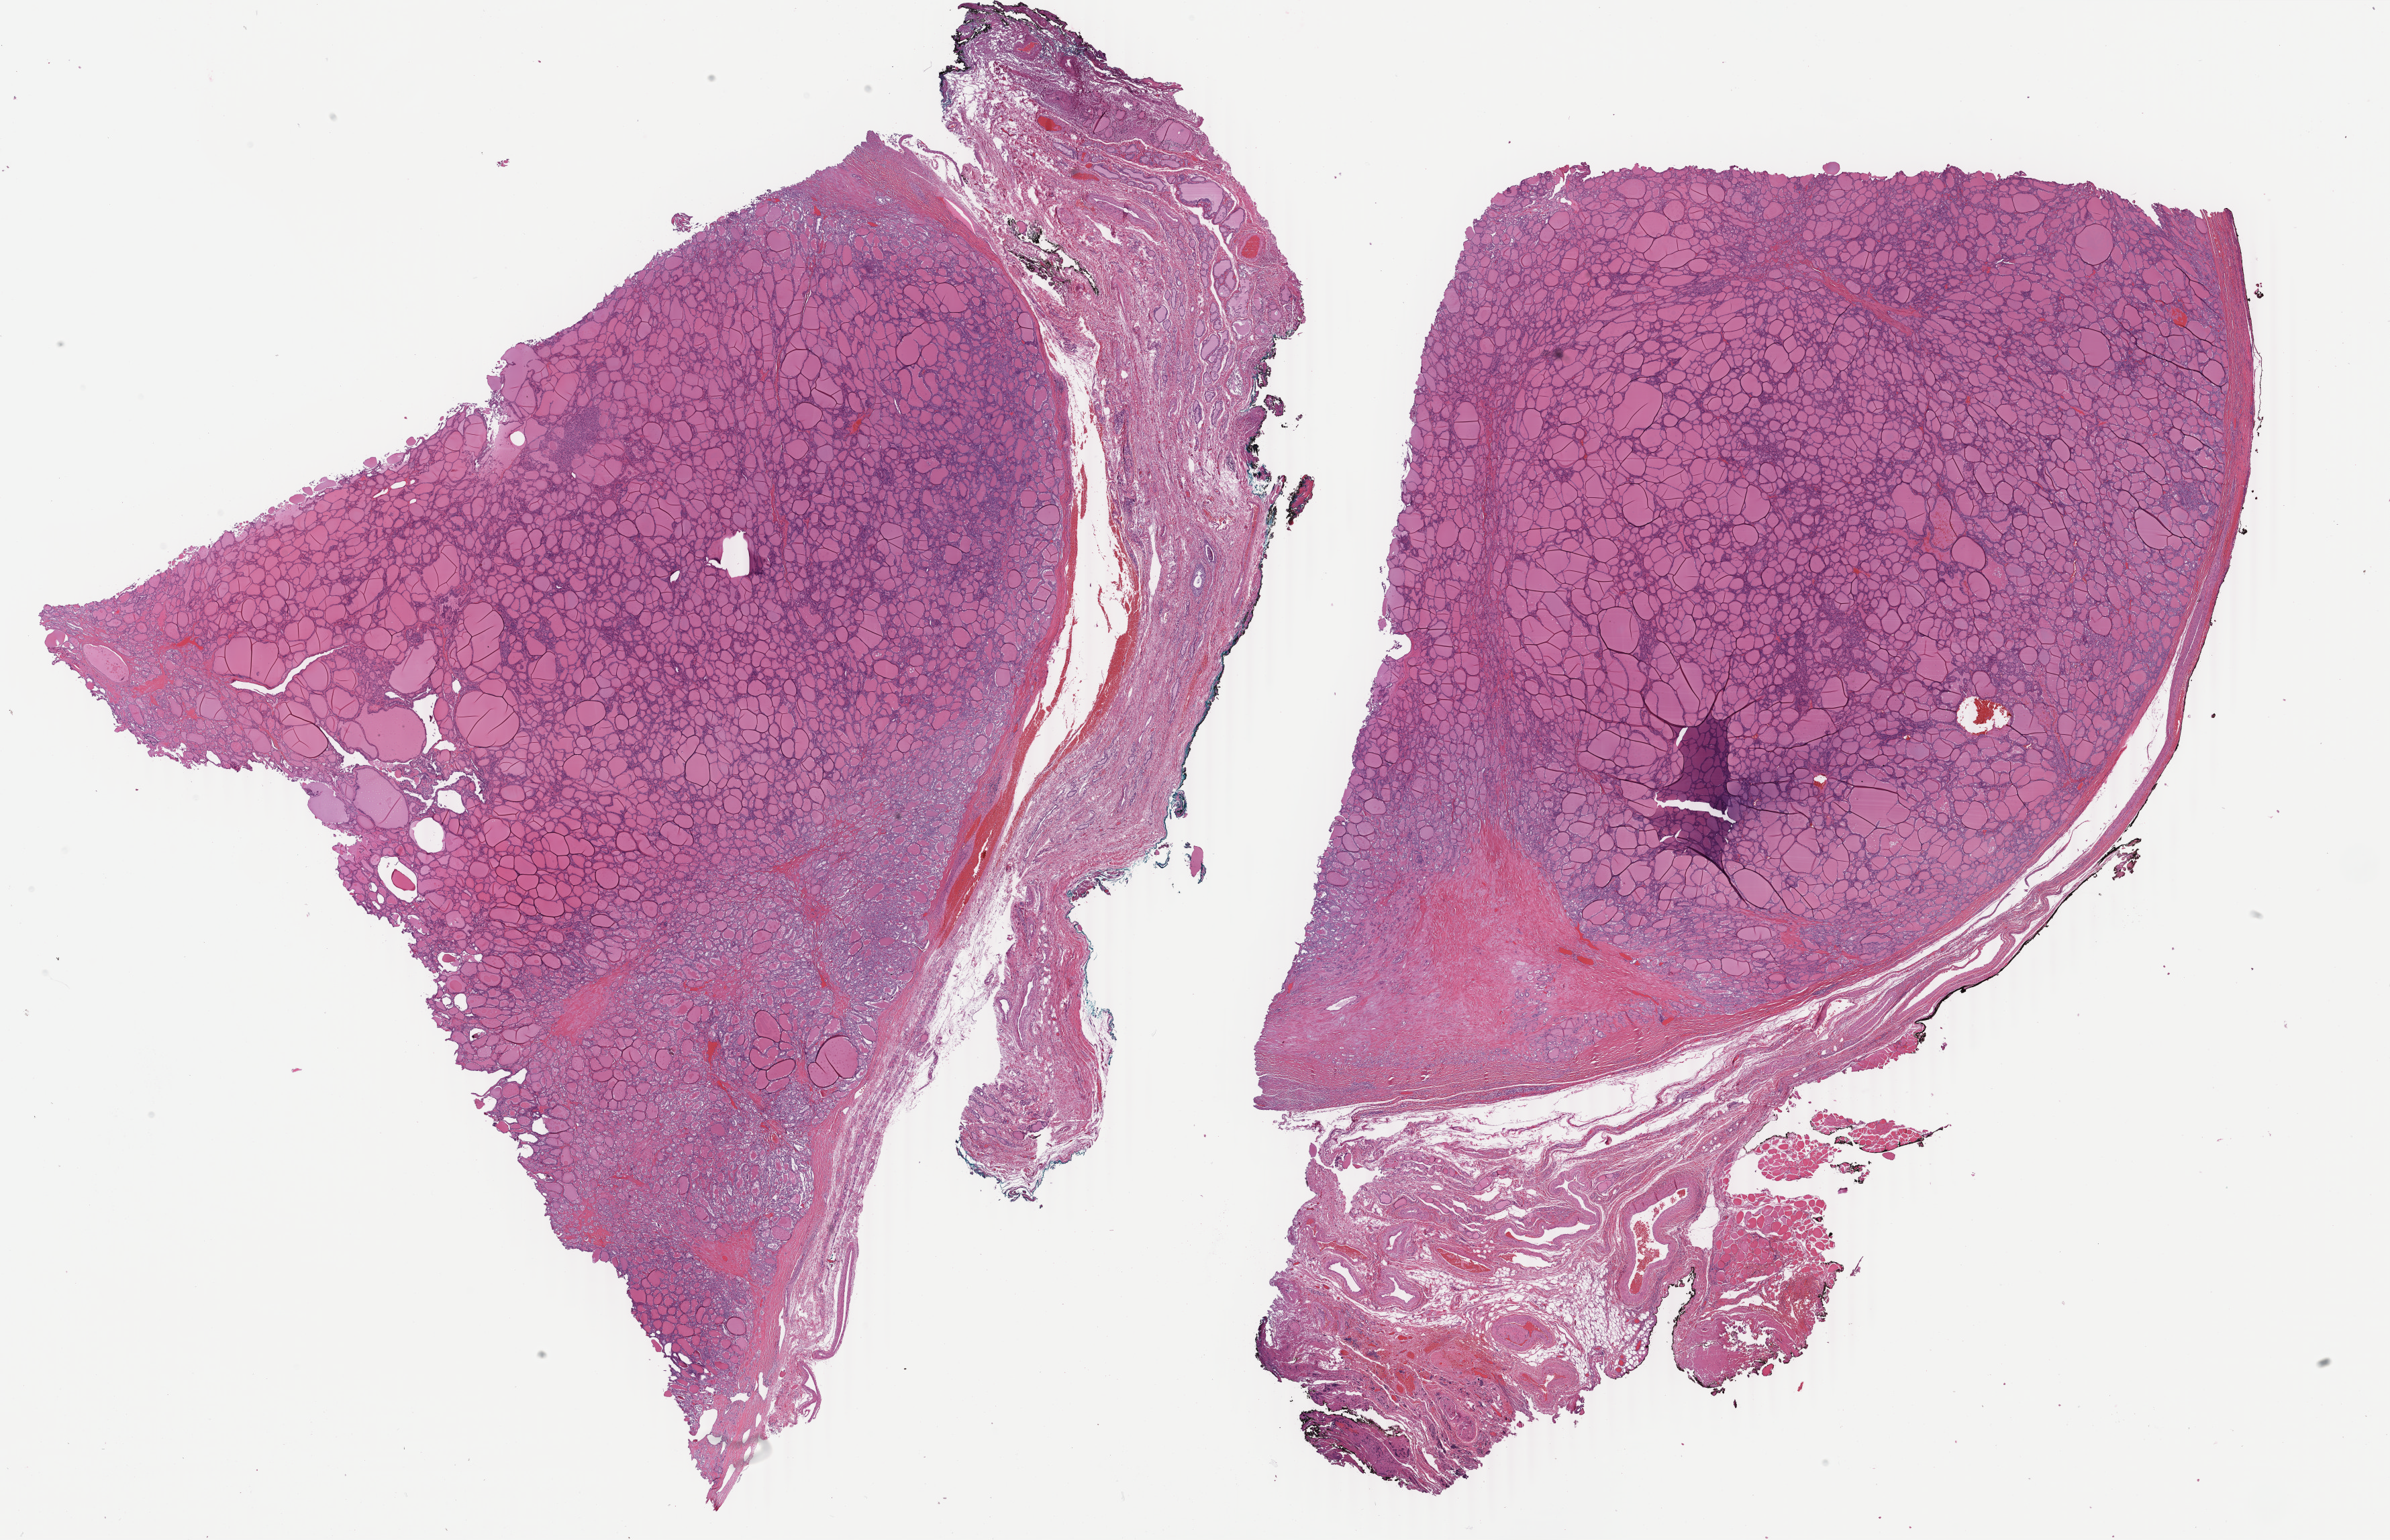
Whole-slide histology image, H&E — low-resolution overview of the scanned area, about 28.3 x 18.2 mm (from a 40x scan), formalin-fixed paraffin-embedded (FFPE) diagnostic section, sample: primary tumour, thyroid. Female patient; age at initial diagnosis 49 years.
Pathologic diagnosis: Papillary carcinoma, follicular variant (thyroid gland).